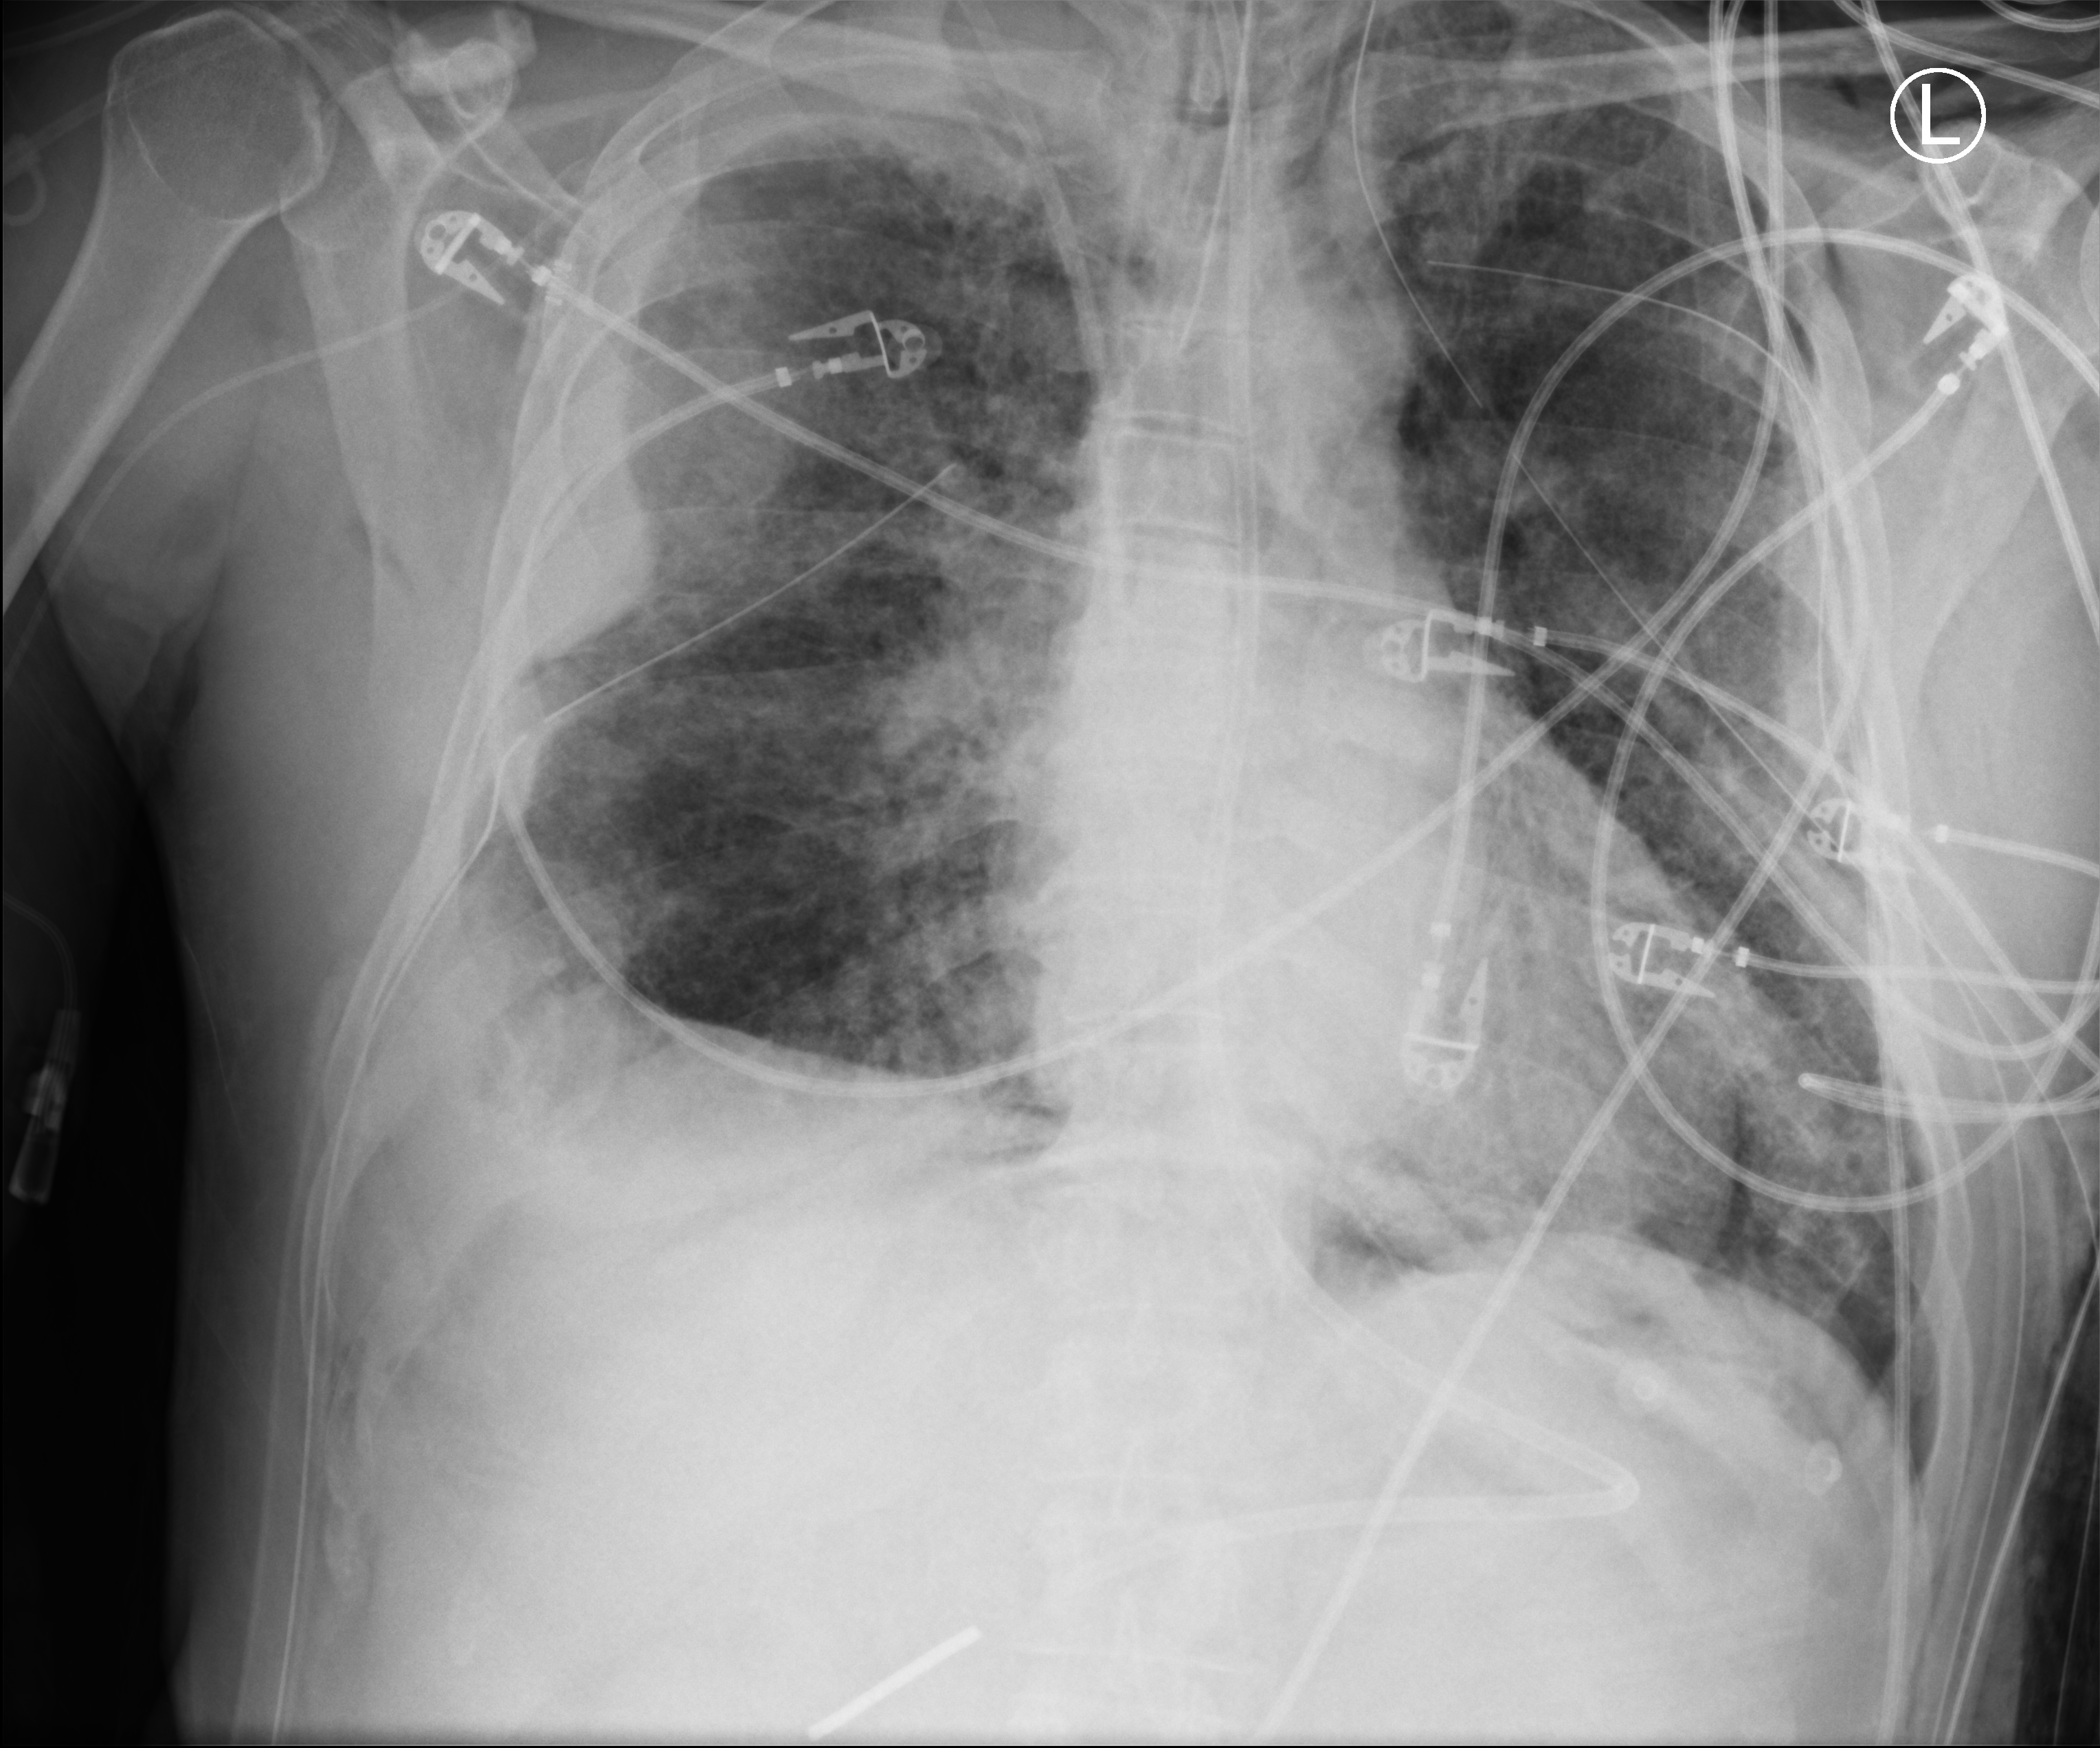
Chest X-ray (portable); anteroposterior (AP) projection. Male patient hospitalised with COVID-19, age 18–59 years.
Hospital-stay facts (about this admission, not read from this image; timing relative to this image not recorded): mechanically ventilated during this hospital stay: yes; length of hospital stay: 42 days.